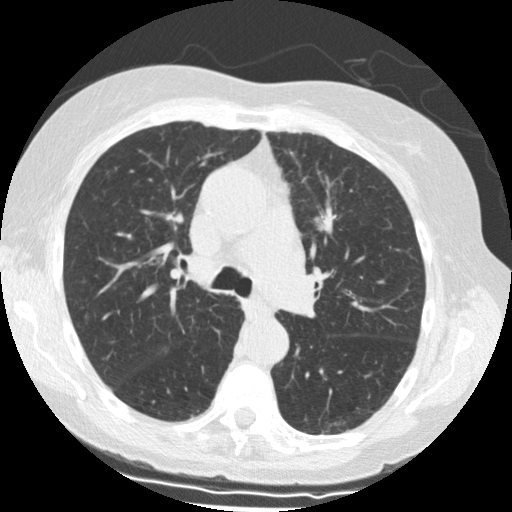
Low-dose screening chest CT, axial slice. Baseline annual screen. Lung window (W 1500 / L -600 HU). Standard (soft-tissue) reconstruction kernel (STANDARD). Slice 48 of 139 in the series. 512 × 512 image matrix. Female, age 69 years at enrolment. Former smoker at enrolment.
Lesion marked by an expert reader, box from (x=299, y=205) to (x=347, y=248) px. The screening reader recorded 2 non-calcified nodules or masses ≥4 mm on this exam (left upper lobe, left upper lobe); which of them this box marks is not recorded. Lung cancer was diagnosed 18 days after this screen: squamous cell carcinoma, NOS, left upper lobe, stage IIIA (AJCC 6th edition), 15 mm at pathology.